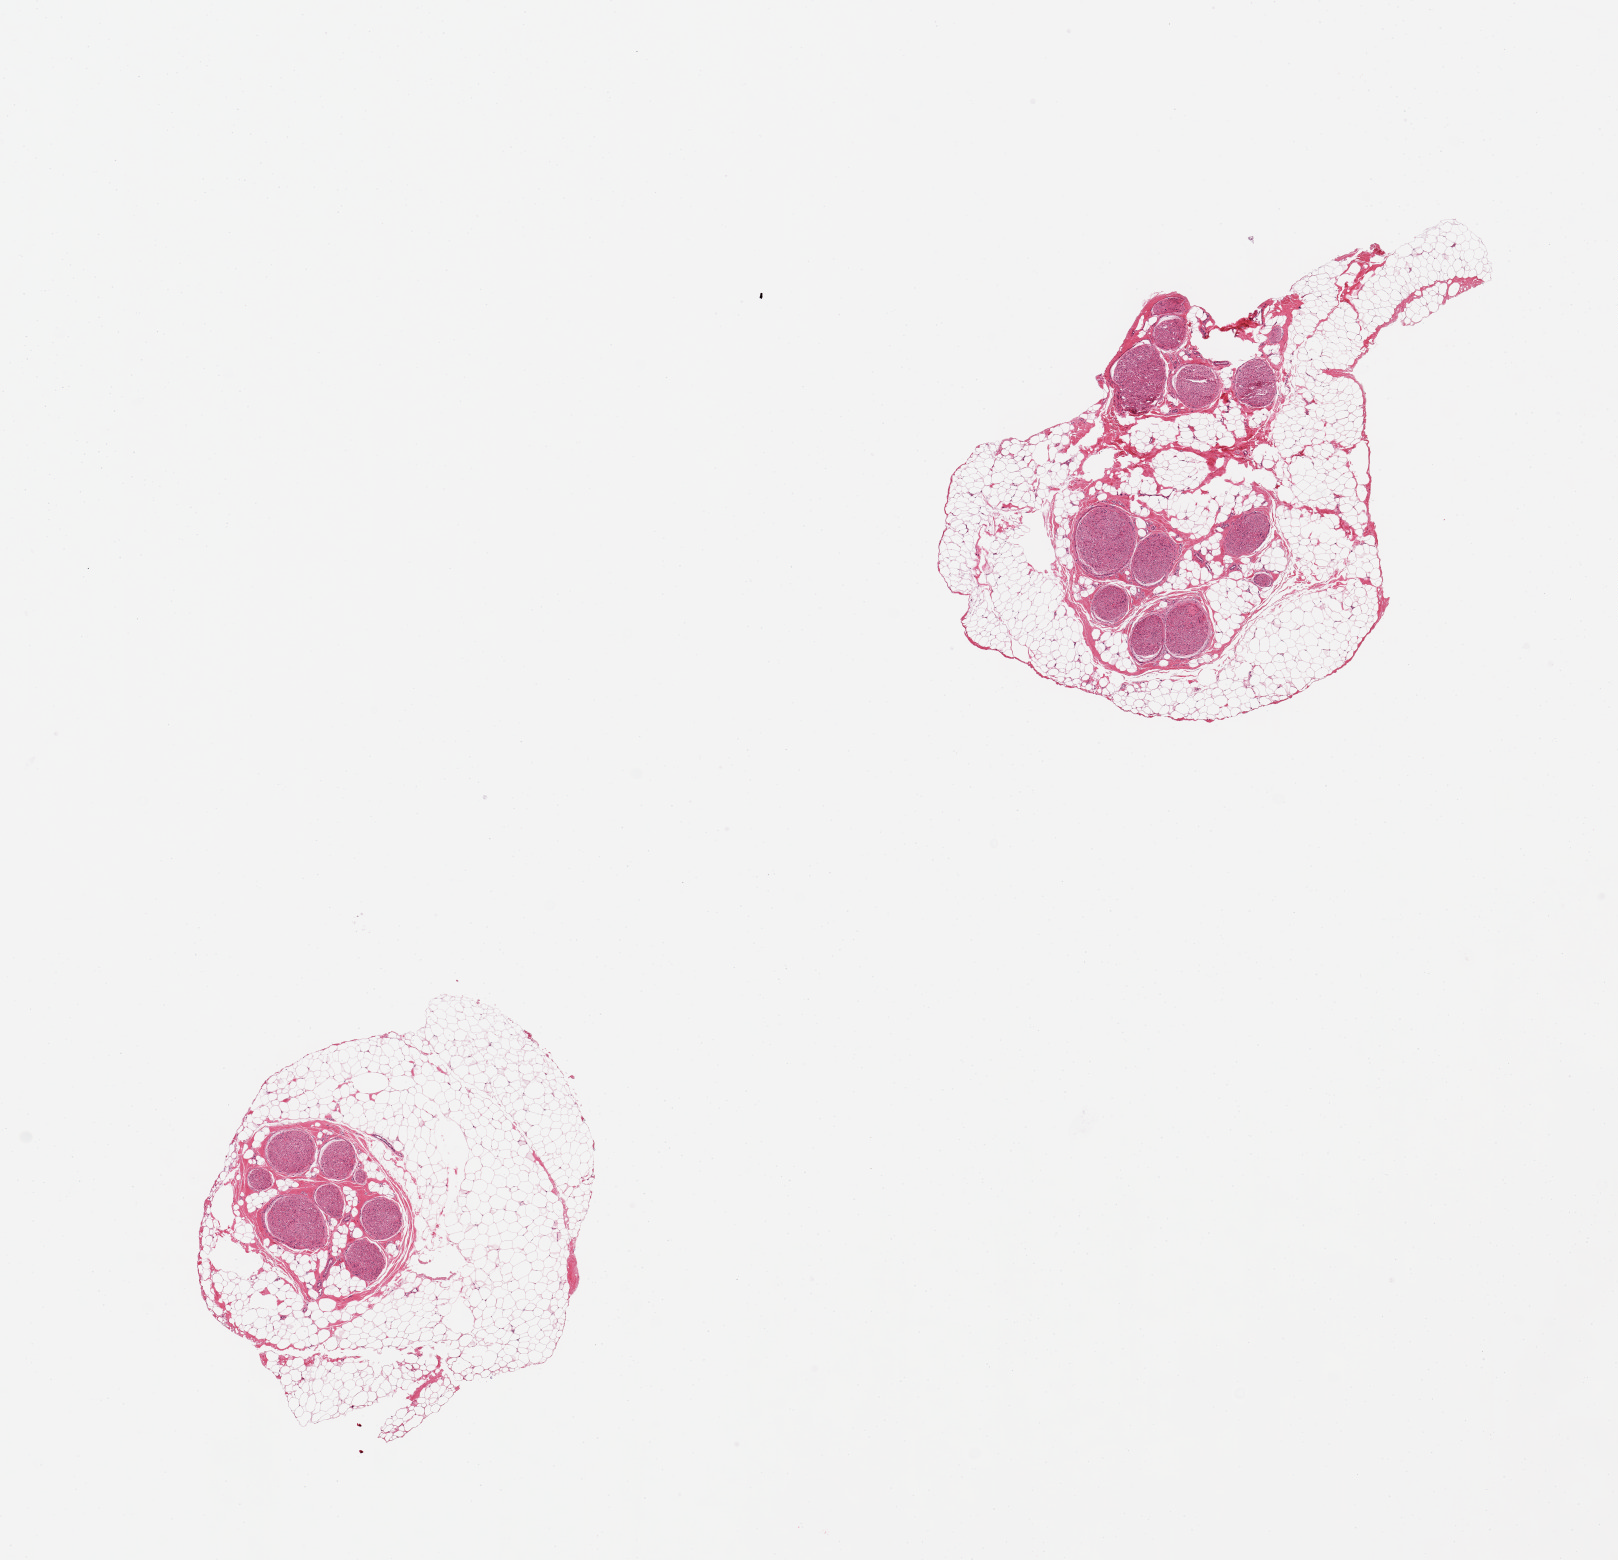
Whole-slide image, hematoxylin and eosin (H&E) stain — shown as a low-resolution overview of the whole scanned area (about 12.8 x 12.3 mm). PAXgene-fixed paraffin-embedded (PFPE) section. Target tissue: tibial nerve. Tissue donor sample.
• reviewer comment on this tissue sample: 2 pieces ~1.5mm d. NOTE: up to 1-1.5mm layer of adherent fat